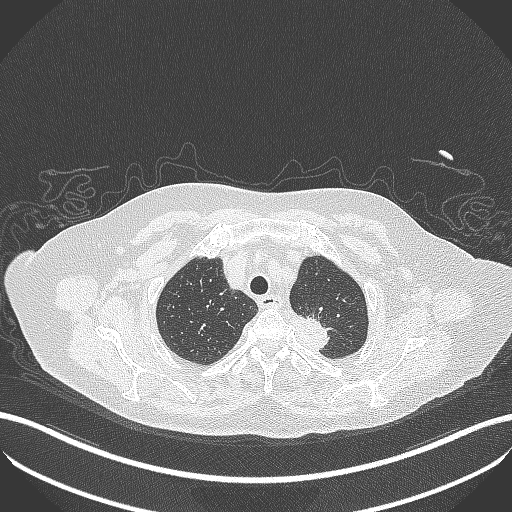
Chest CT, one axial slice; reconstruction kernel B70f; lung window (W 1500 / L -600 HU); 1 mm slice thickness; 512 × 512 image matrix, field of view 400 × 400 mm. Patient: female, 81 years. Case-level facts recorded for this patient, not image findings: clinical TNM (as recorded): T2a N0 M0.
Annotated regions visible in this slice (bounding box drawn by a radiologist):
- lung tumour (recorded histology: adenocarcinoma): bounding box (x1, y1, x2, y2) in pixels: (285, 310, 340, 358)